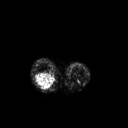
FDG PET of an extremity soft-tissue mass (from a PET/CT study), one axial slice; 3.27 mm slice thickness; 128 × 128 image matrix, field of view 500 × 500 mm. Patient: female, 62 years. Case-level facts recorded for this patient, not image findings: histological type: liposarcoma; site of the primary tumour: right thigh.
Structures marked on this image (expert contour drawn on MRI and transferred to this co-registered scan by the dataset authors):
- gross tumour volume (mass): bounding box [x1, y1, x2, y2] px = [35, 72, 56, 90]